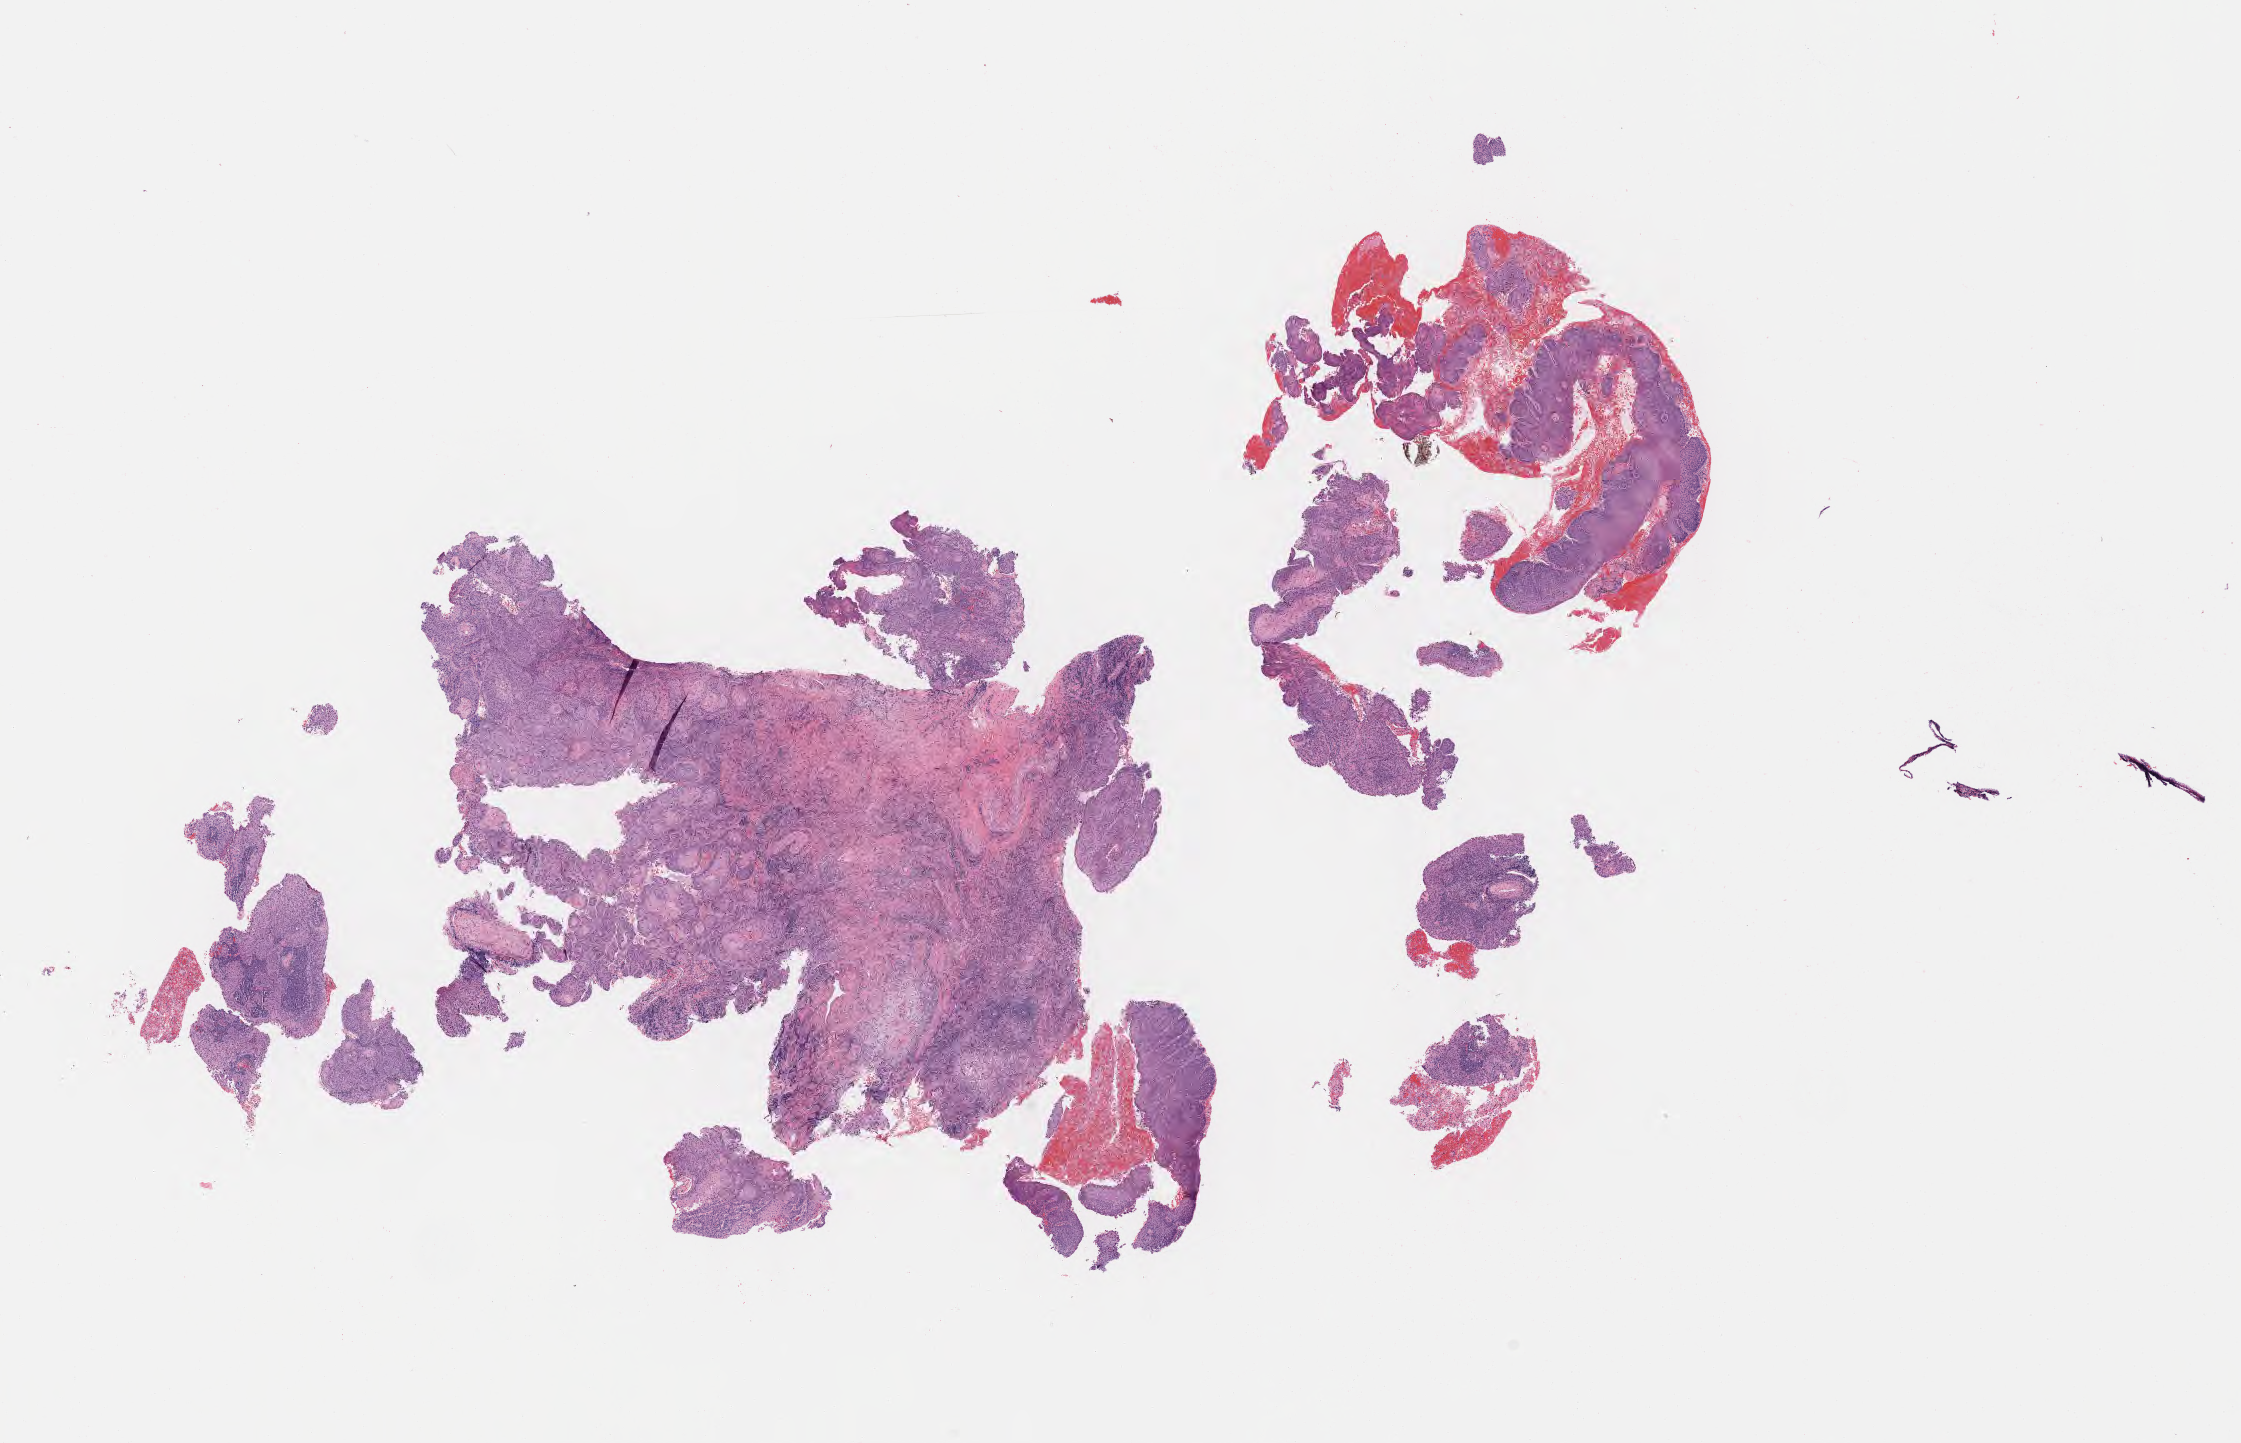
Digitized haematoxylin and eosin-stained section, shown as a low-resolution overview of the whole scanned area (about 18.1 x 11.7 mm); specimen: tumor tissue; site: cervix. Female patient, aged 60.
Diagnosis: Squamous cell carcinoma, keratinizing, NOS.